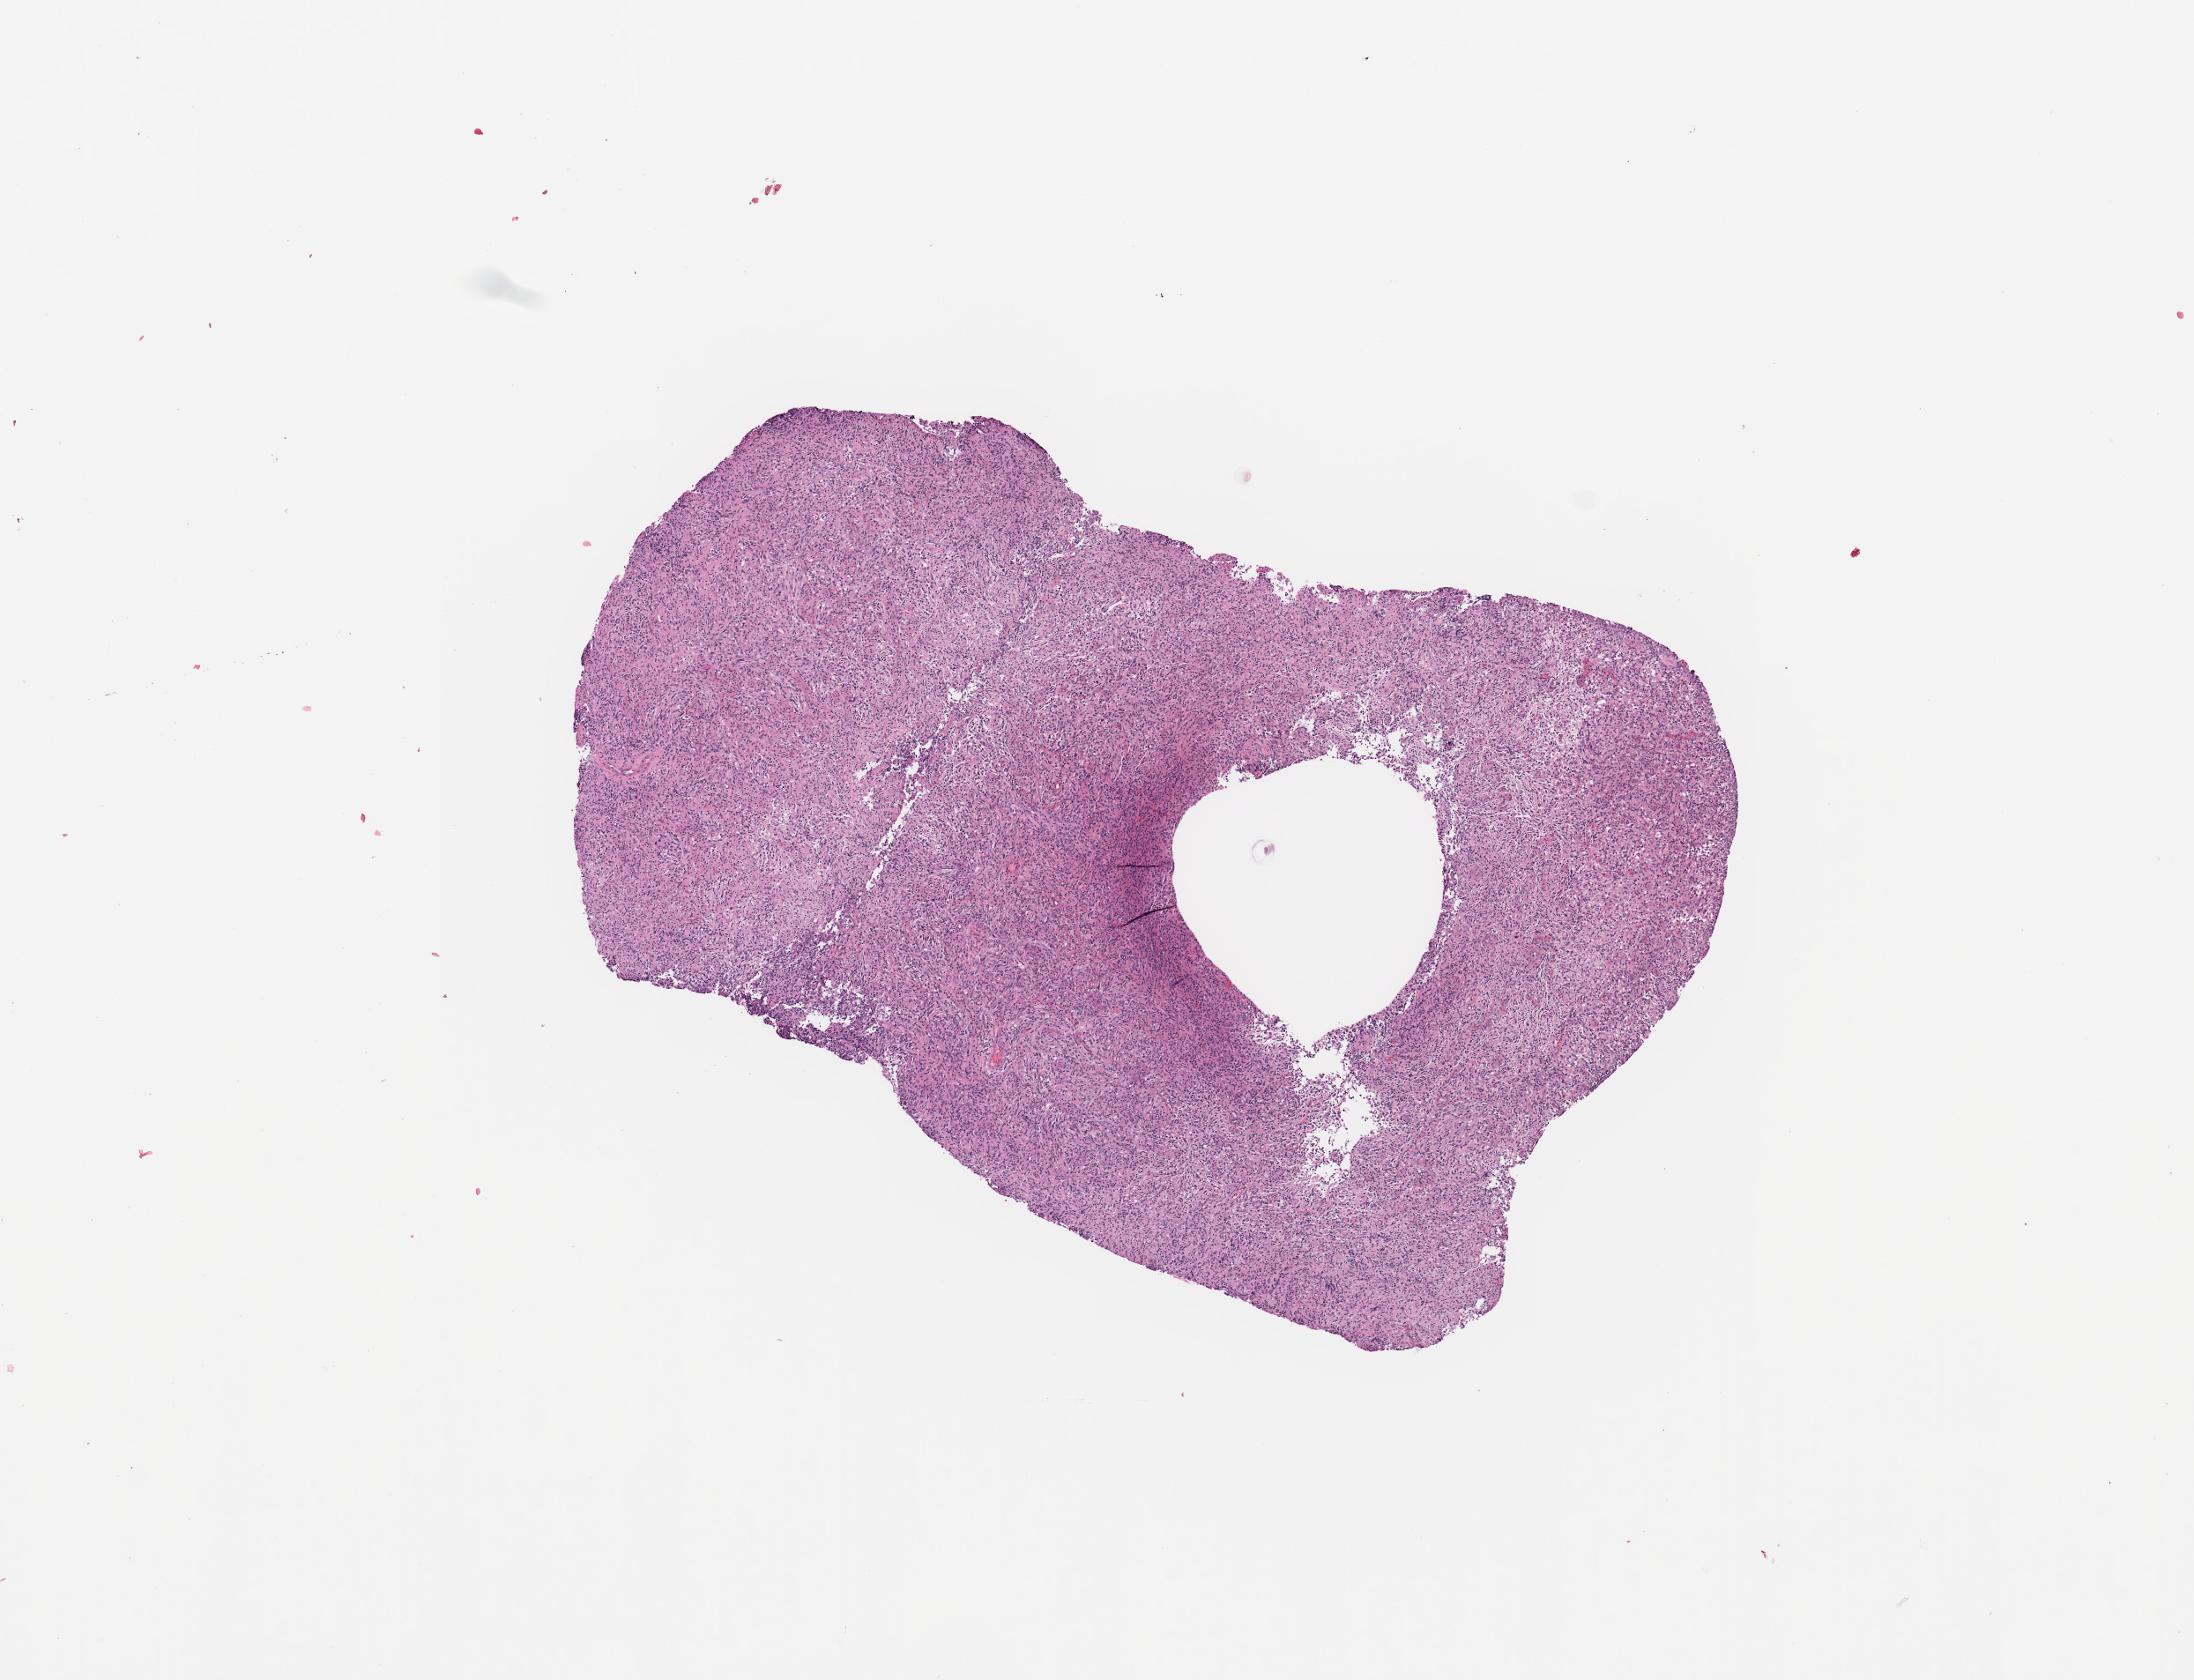
Whole-slide histology image, Hematoxylin and eosin (H&E) stained, a low-resolution overview of the entire scanned area, about 9.8 x 7.5 mm (acquisition: 20x scan). Tumour tissue sample, sampled site: frontal lobe. Female, 42 y/o. Composition of this section per pathologist review: tumour nuclei 85%, necrosis 5%.
Diagnosis: Glioblastoma.